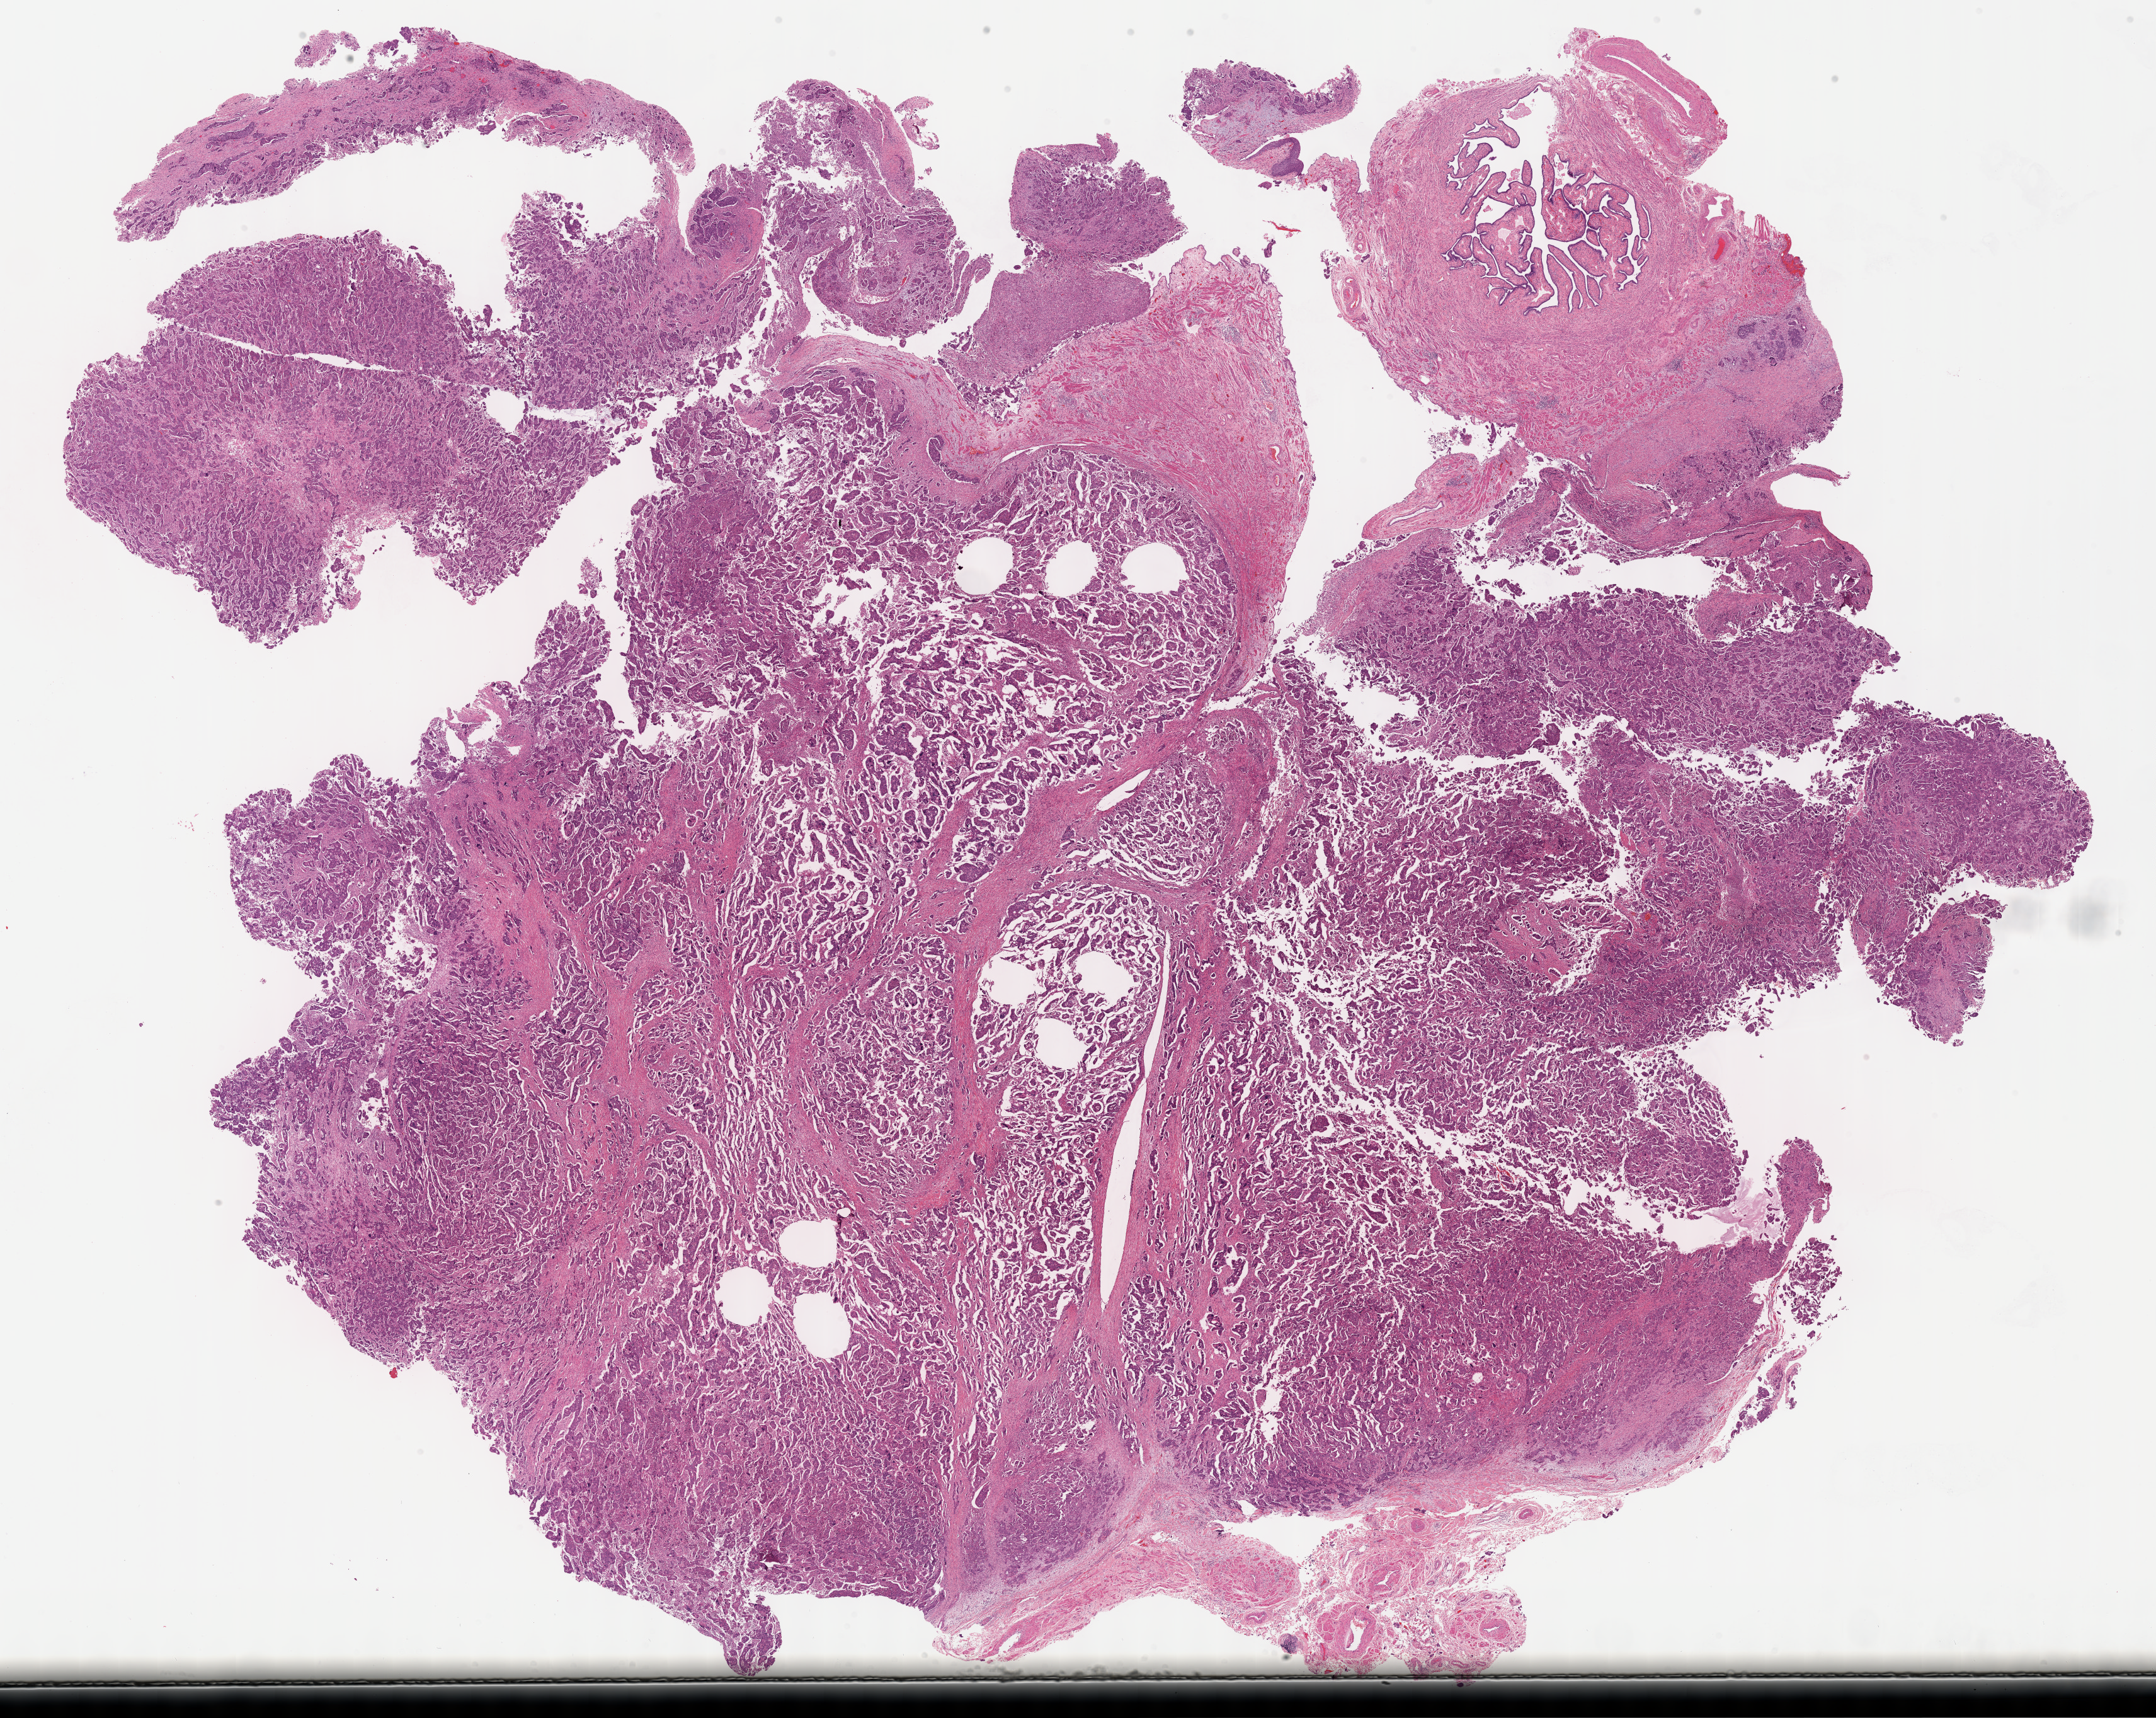
H&E whole-slide image, shown as a low-resolution overview of the whole scanned area (about 27.7 x 22.1 mm, from a 40x scan), formalin-fixed paraffin-embedded (FFPE) diagnostic section, sample: primary tumour, ovary. Female, age 83 years at initial diagnosis. Histologic grade: G3 (poorly differentiated).
FIGO stage: IIIC. Pathologic diagnosis: Serous cystadenocarcinoma, NOS.